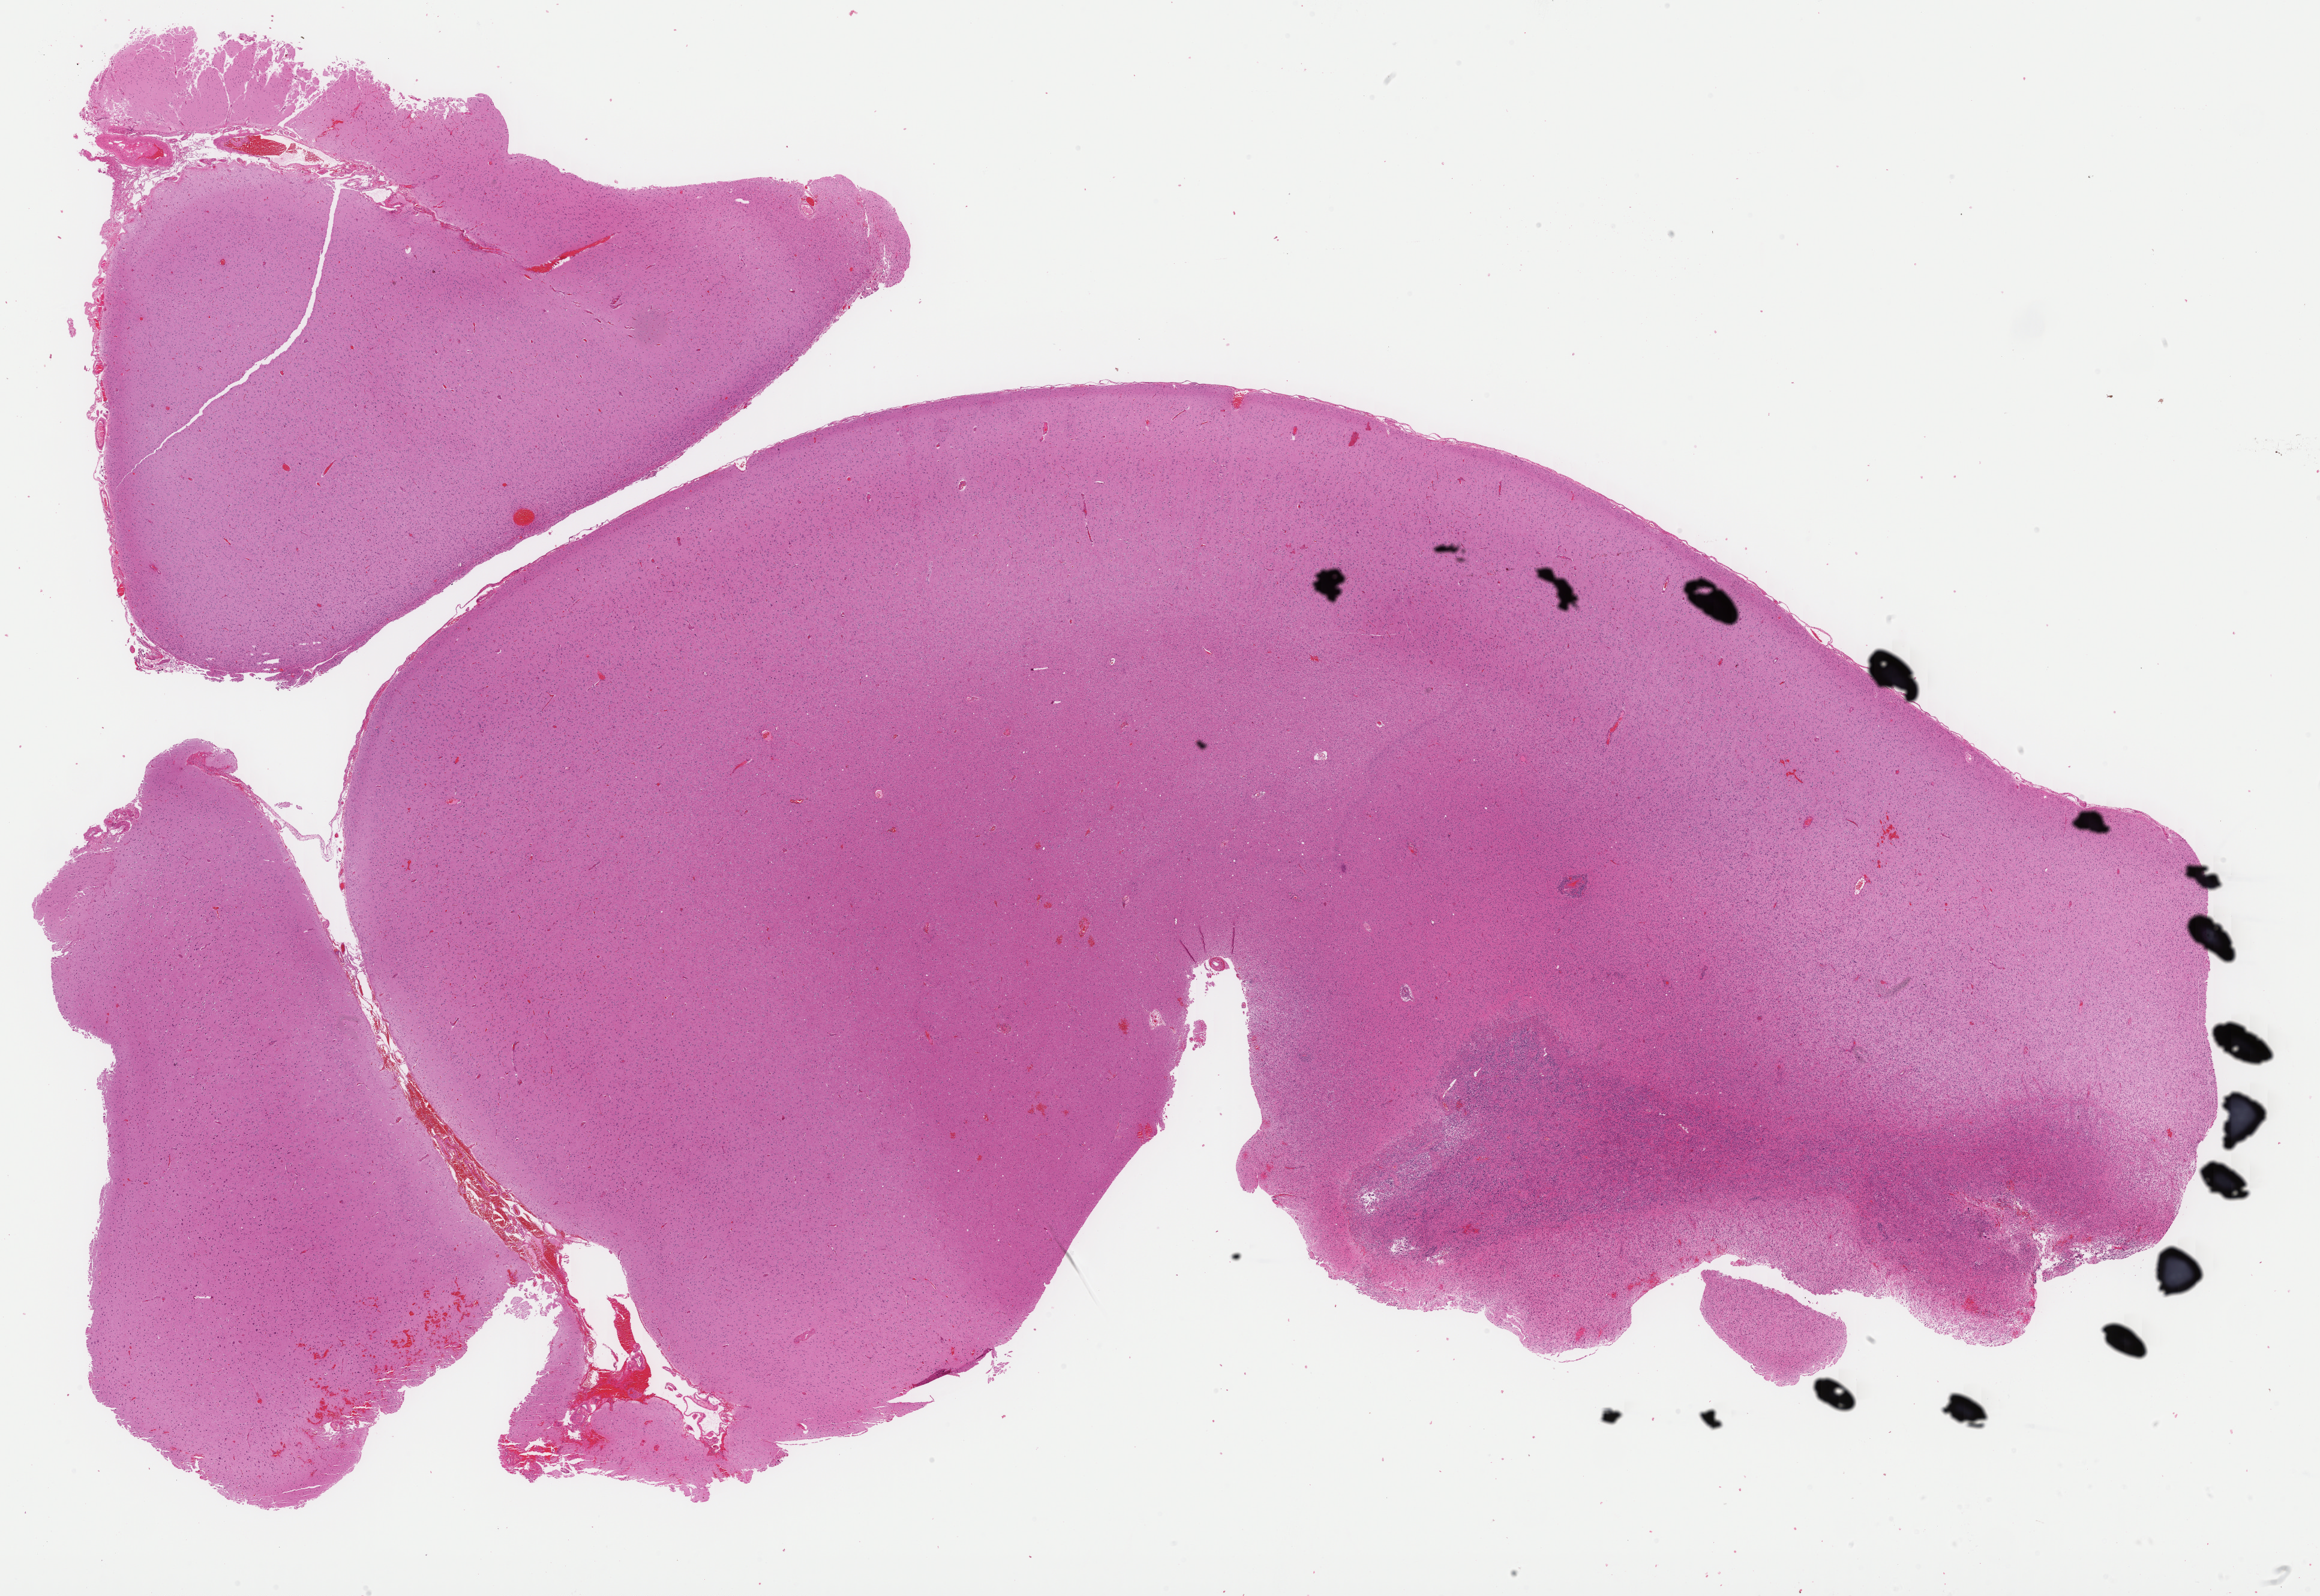
Digitized H&E tissue section (whole slide), whole scanned area (about 30.5 x 21.0 mm, from a 40x scan) shown as a low-resolution overview, formalin-fixed paraffin-embedded (FFPE) diagnostic section, sample: primary tumour, brain. Patient: female, age at initial diagnosis 38 years. Histologic grade: G3 (poorly differentiated).
- diagnosis: Mixed glioma (cerebrum)